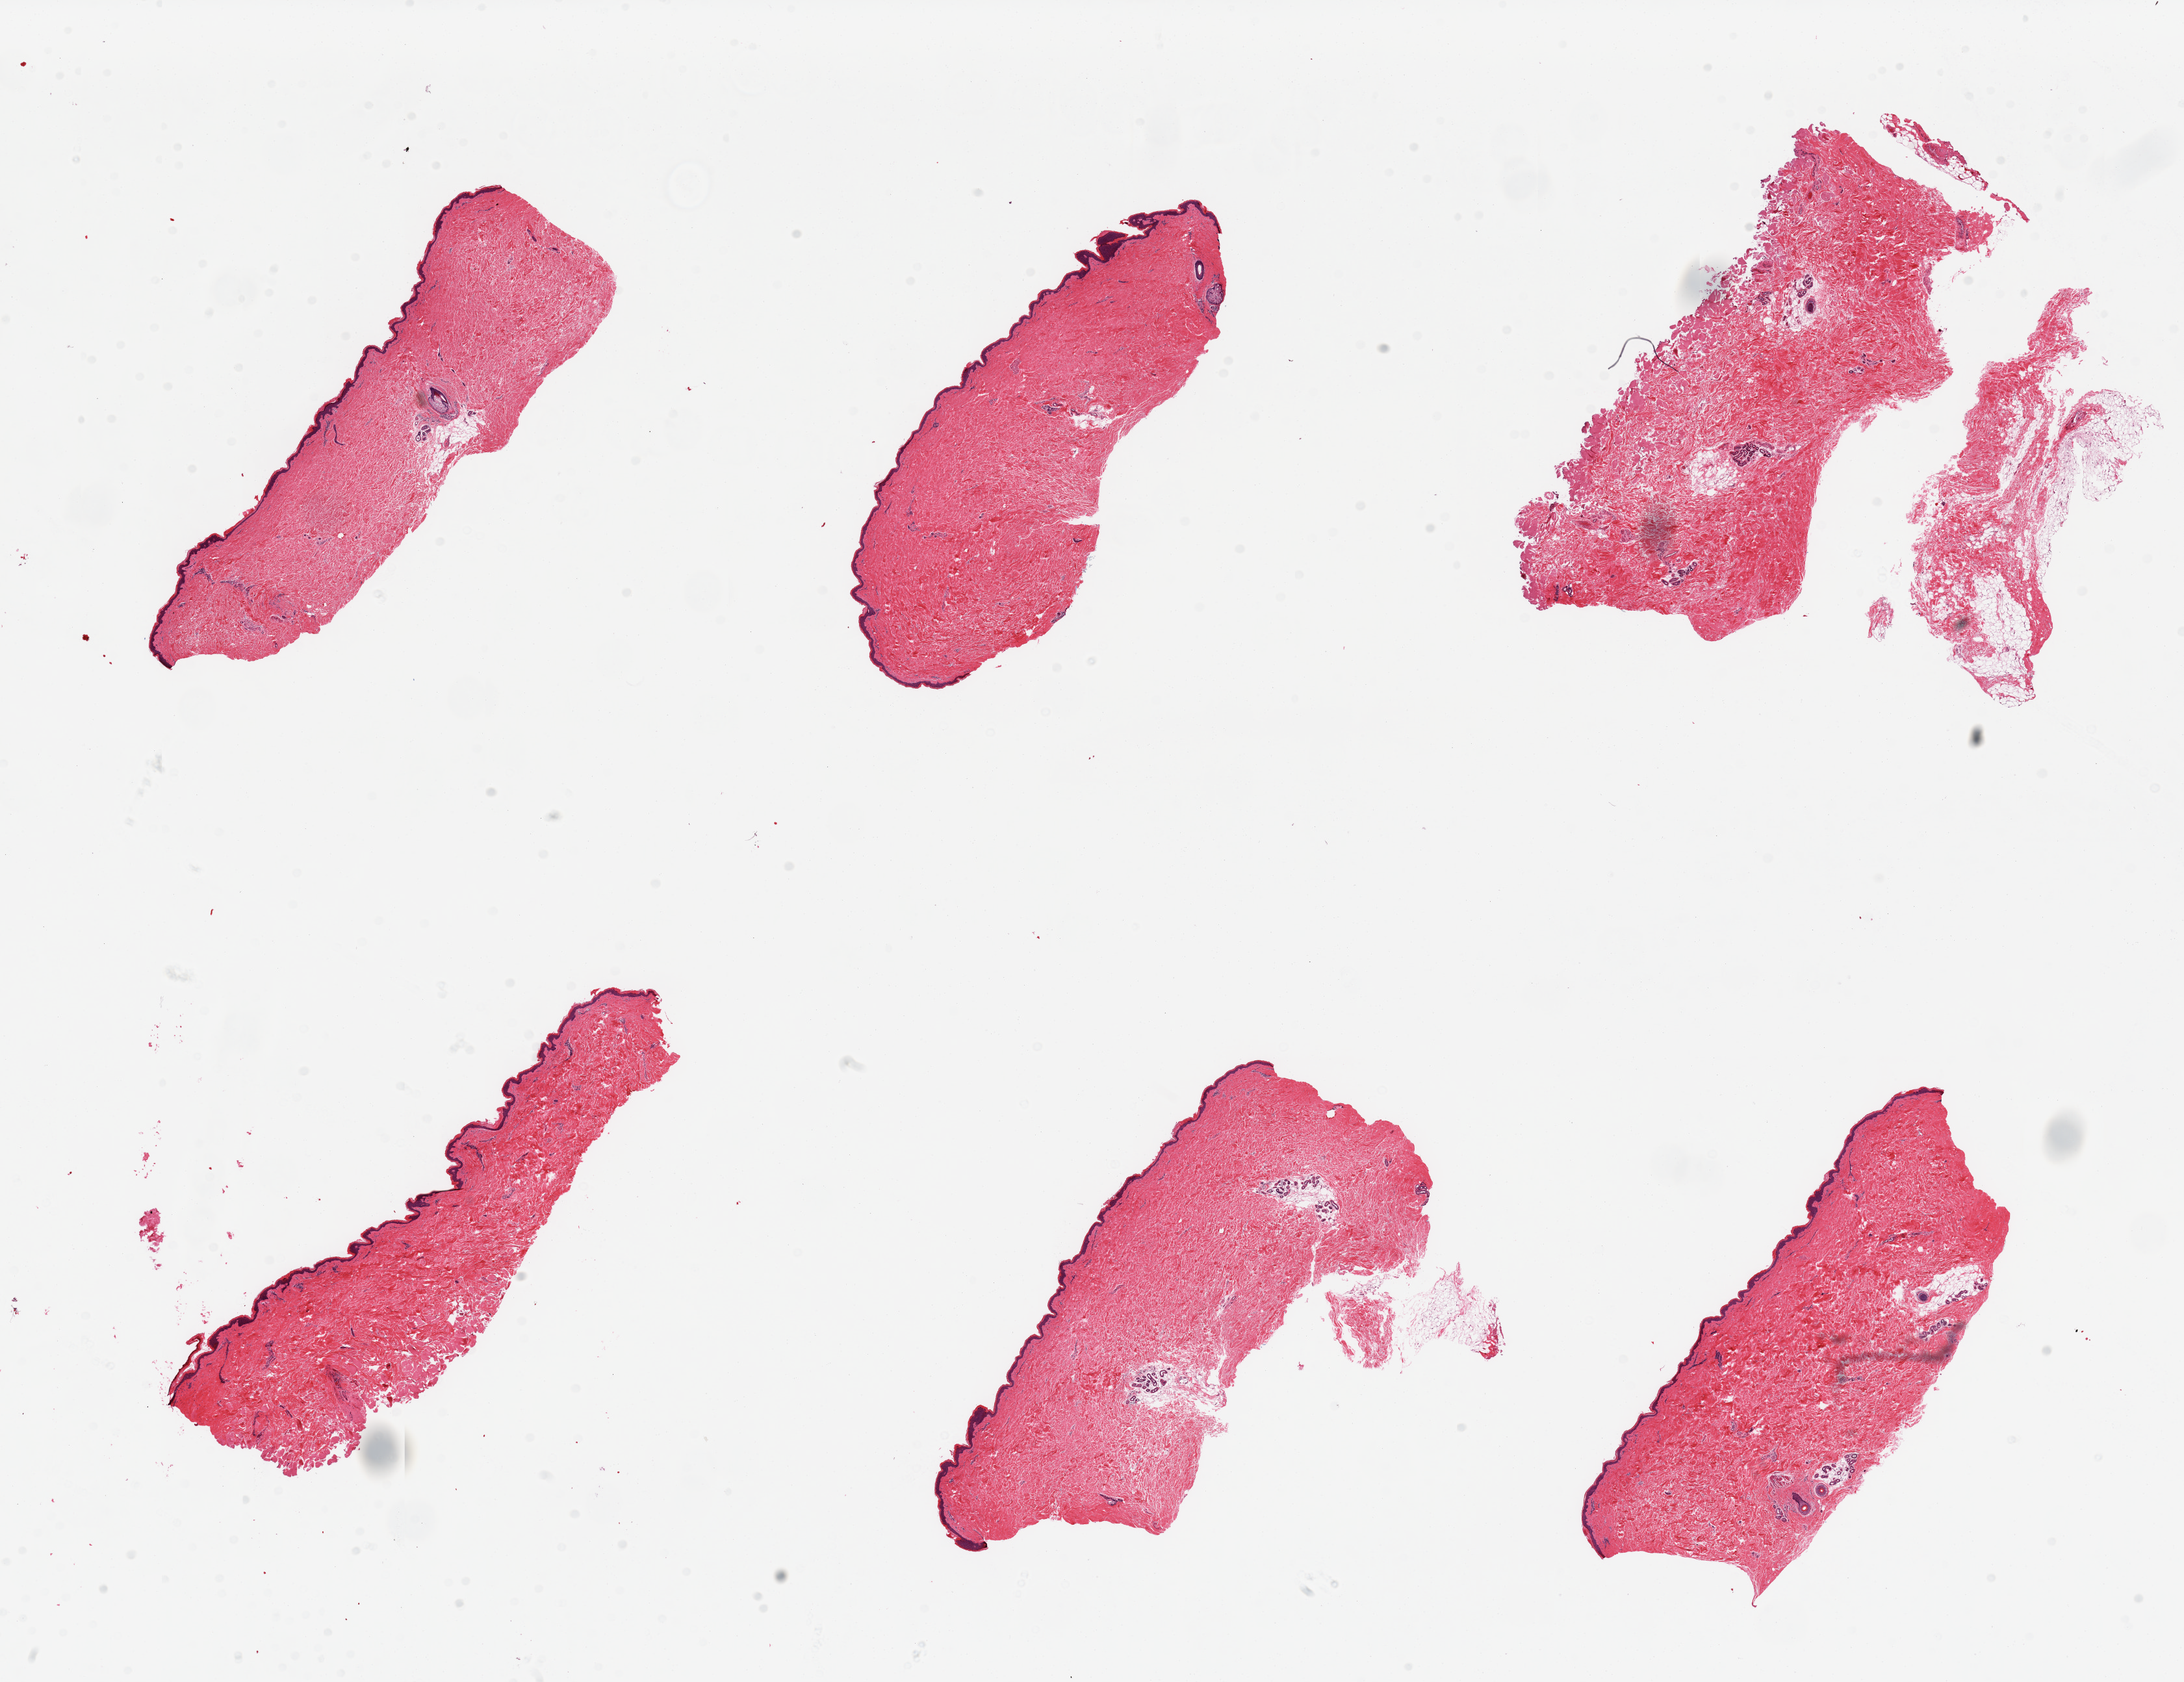
Whole-slide image, H&E stain — shown as a low-resolution overview of the whole scanned area (about 26.6 x 20.5 mm, slide scanned at 20x). PAXgene-fixed paraffin-embedded (PFPE) section. Section of skin of suprapubic region (target tissue). Donor tissue sample.
Pathologist's review note for this sample: 6 pieces; 1 piece without epidermis (in this section).